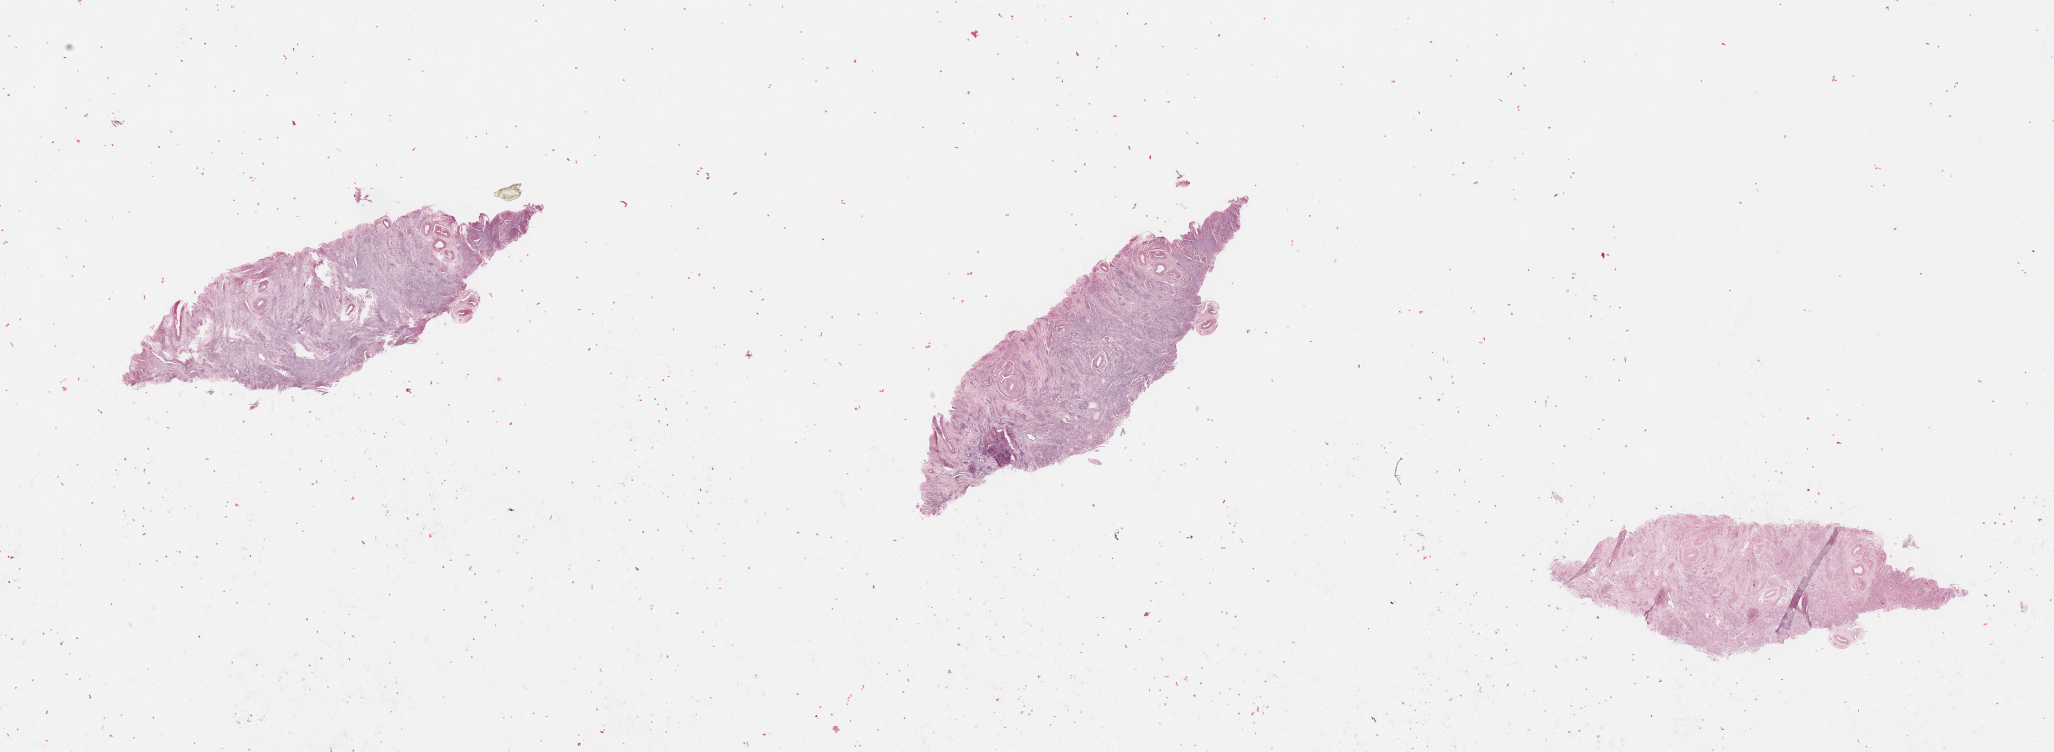
H&E-stained whole-slide image, whole scanned area (about 32.5 x 11.9 mm, acquisition: 20x scan) shown as a low-resolution overview; normal (non-tumour) tissue sample, uterus. 53-year-old female patient.
This section: normal (non-tumour) tissue from the same patient. Patient diagnosis: Endometrioid adenocarcinoma, NOS.